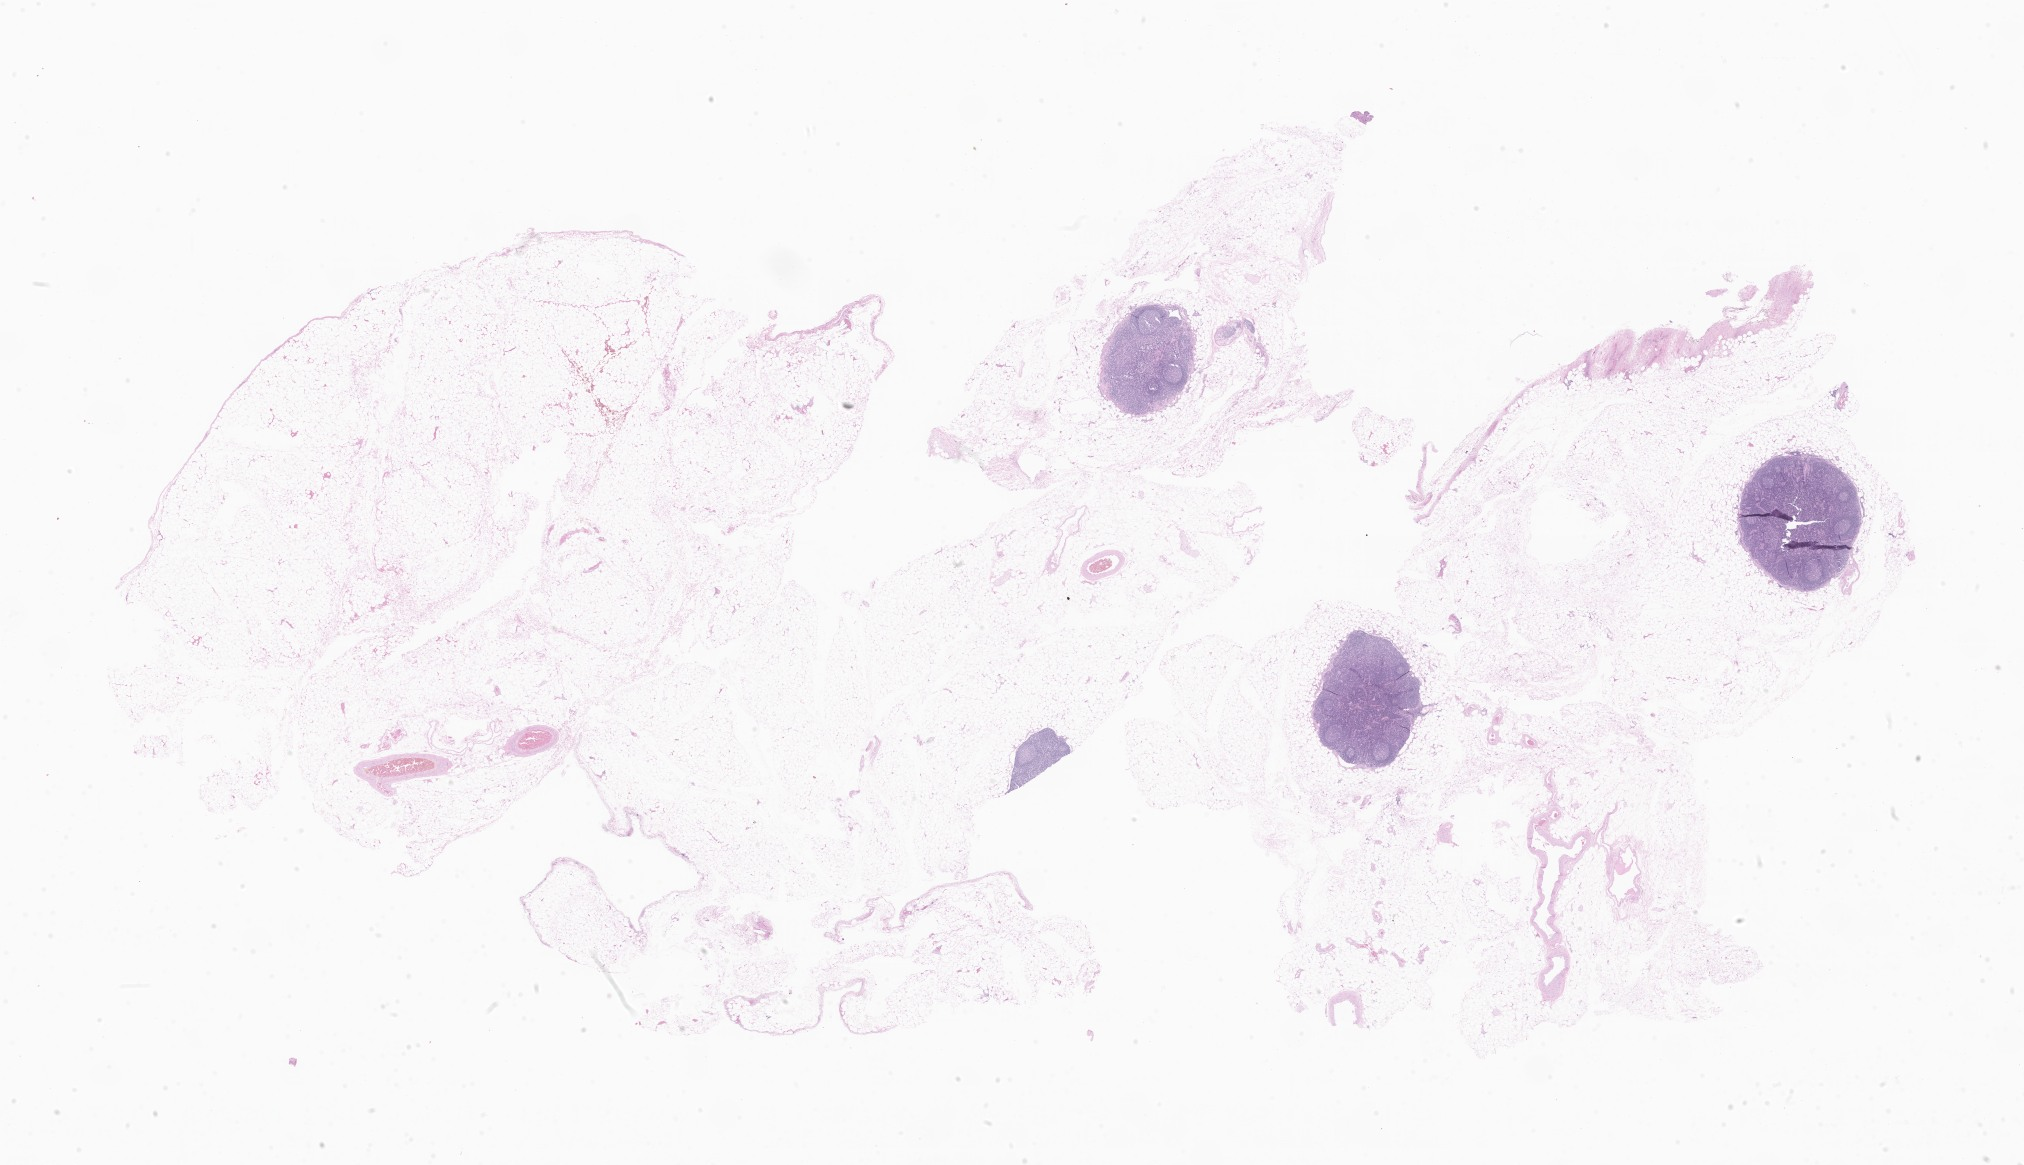
Digitized H&E-stained section — shown as a low-resolution overview of the whole scanned area (about 34.1 x 19.6 mm); formalin-fixed, paraffin-embedded (FFPE) tissue; normal-tissue sample (non-tumor) from a patient with adenocarcinoma, NOS; site: rectum. Patient: male, age at initial diagnosis 65 years. Pathologist review of this section (percent, as recorded): tumor cells 0%, tumor nuclei 0%, stromal cells 100%, necrosis 0%, normal cells 0%. Inflammatory infiltration, as recorded: lymphocyte infiltration 70%, monocyte infiltration 5%, neutrophil infiltration 8%.
- this section: non-tumor tissue sample; the patient's diagnosis is given above